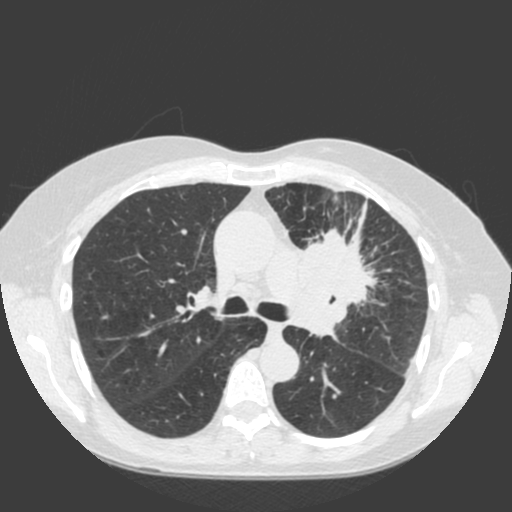
Chest CT (low-dose screening protocol), one axial image, first (baseline) screen, lung window (W 1500 / L -600 HU), slice 63 of 184 in the series. Female, age 66 years at enrolment. Current smoker at enrolment.
Expert reader's lesion annotation, bounding box <280,218,400,326> (left, top, right, bottom; pixels). Reader record for this screening exam (exam-level; its link to the box is not recorded): non-calcified nodule or mass ≥4 mm, left upper lobe, 61 × 45 mm, spiculated (stellate) margins, soft tissue attenuation. Later outcome: lung cancer diagnosed 19 days after this screen — squamous cell carcinoma, keratinizing, NOS, left upper lobe, left hilum, mediastinum, left main stem bronchus, other location, poorly differentiated (G3), stage IIIB (AJCC 6th edition), 60 mm at pathology.